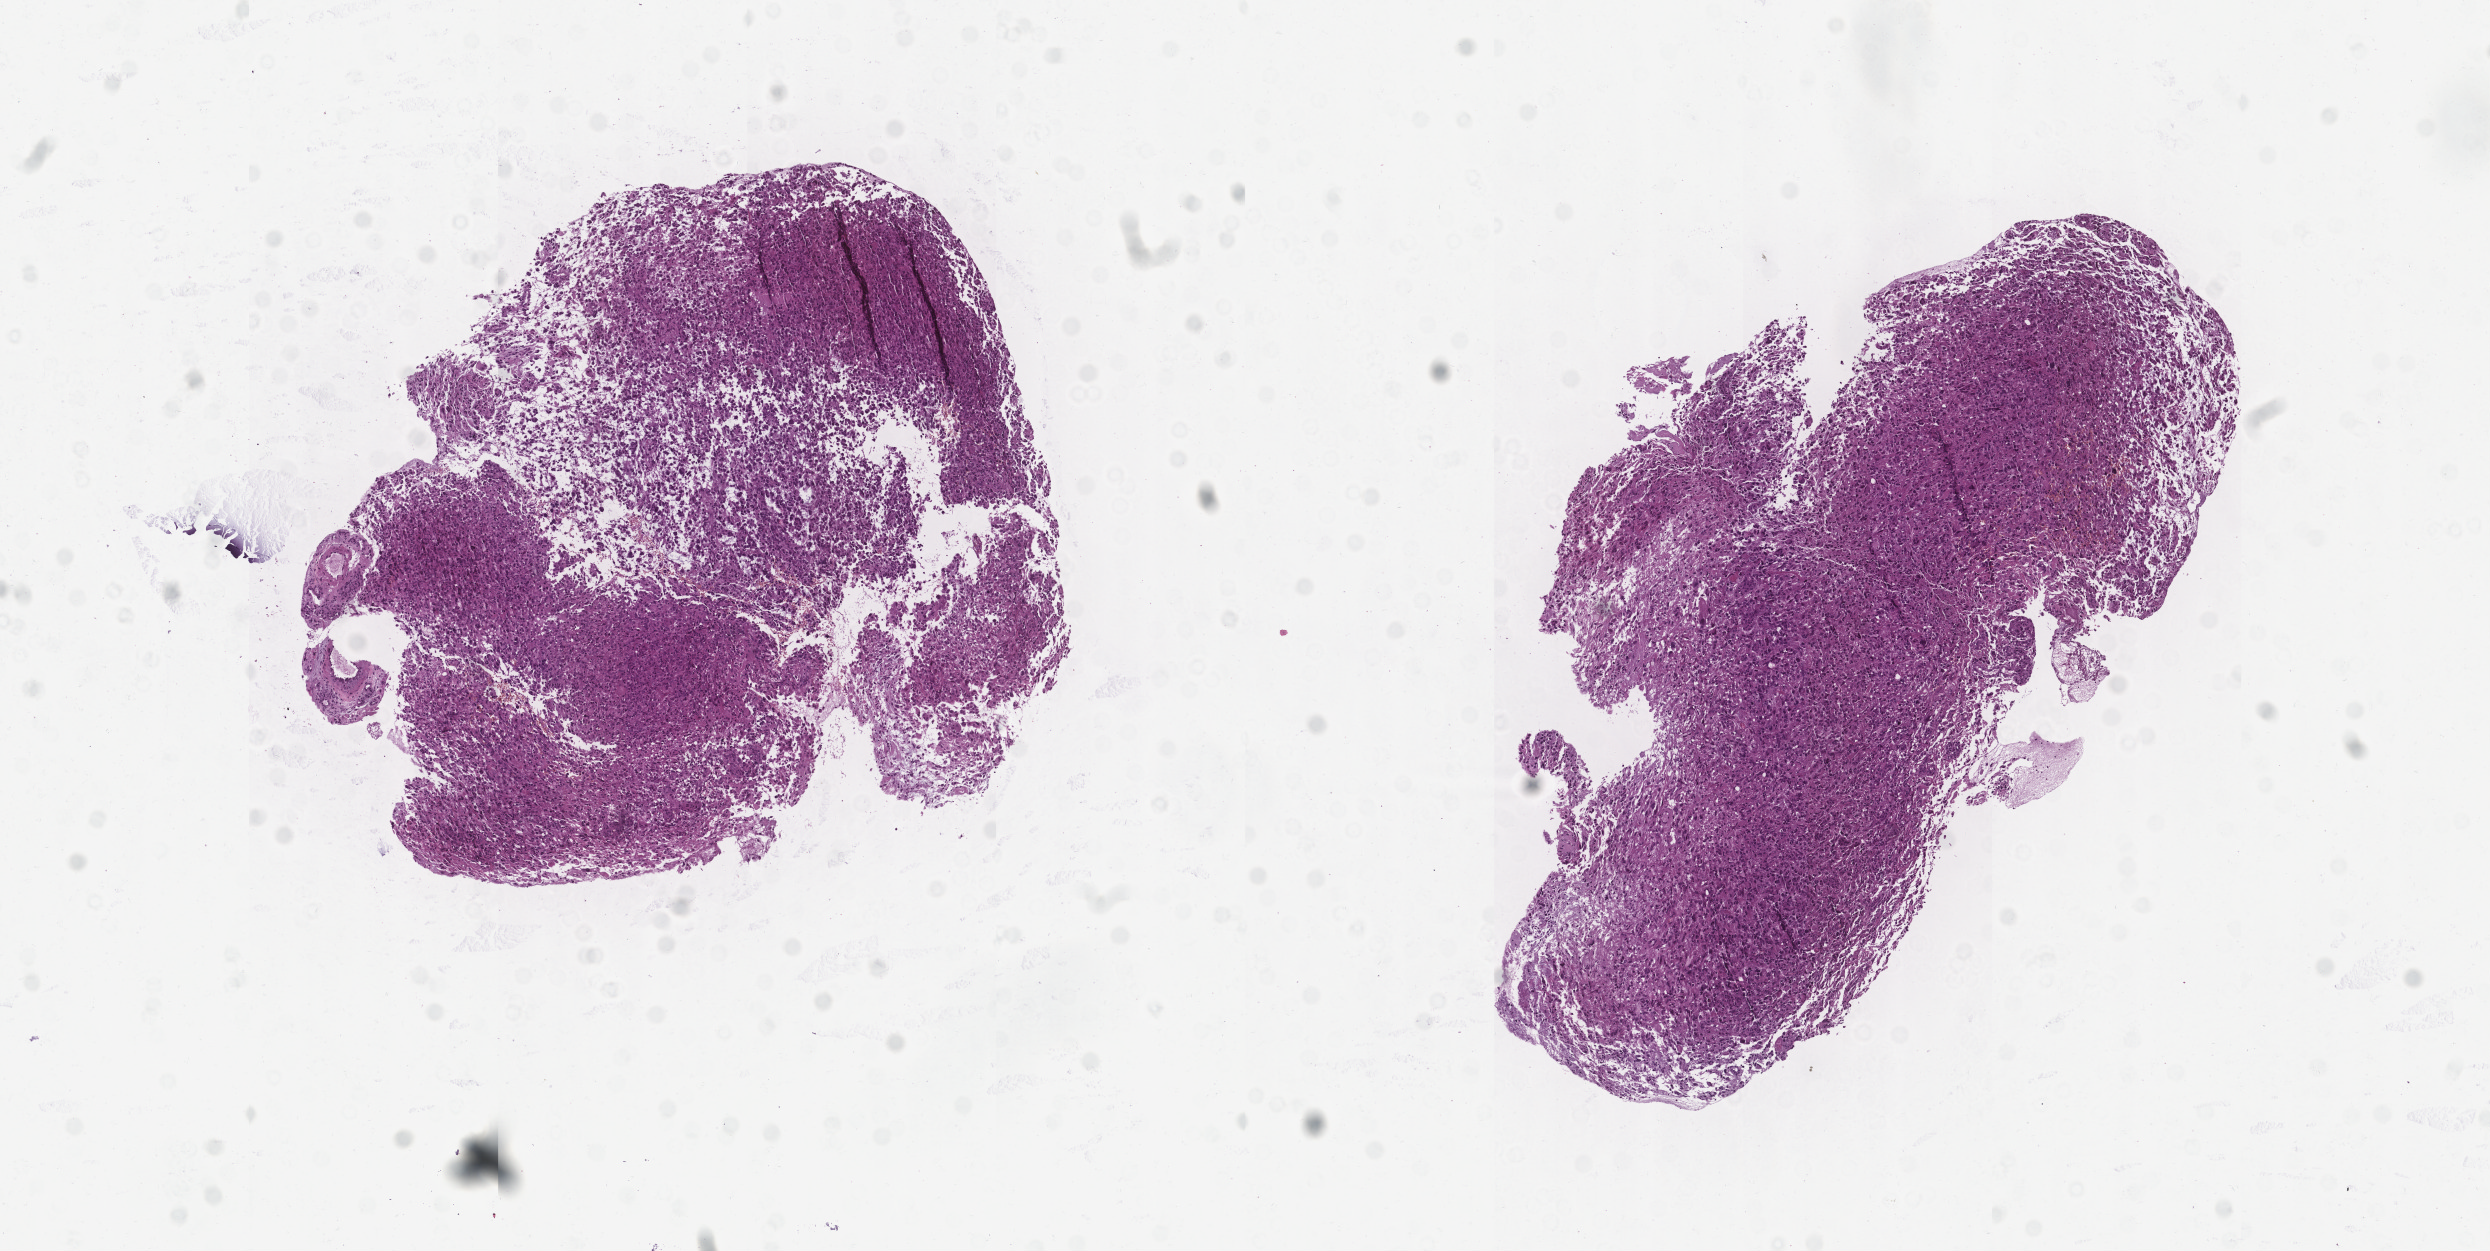
Hematoxylin and eosin (H&E) stained whole-slide image — whole scanned area (about 10.0 x 5.0 mm, from a 20x scan) shown as a low-resolution overview. Tumour tissue sample, sampled site: brain. Patient: male, age 71 years. Pathologist review of this section (percent, as recorded): tumour nuclei 85%, necrosis 5%.
Diagnosis: Glioblastoma. Primary tumour site (as recorded): temporal lobe.